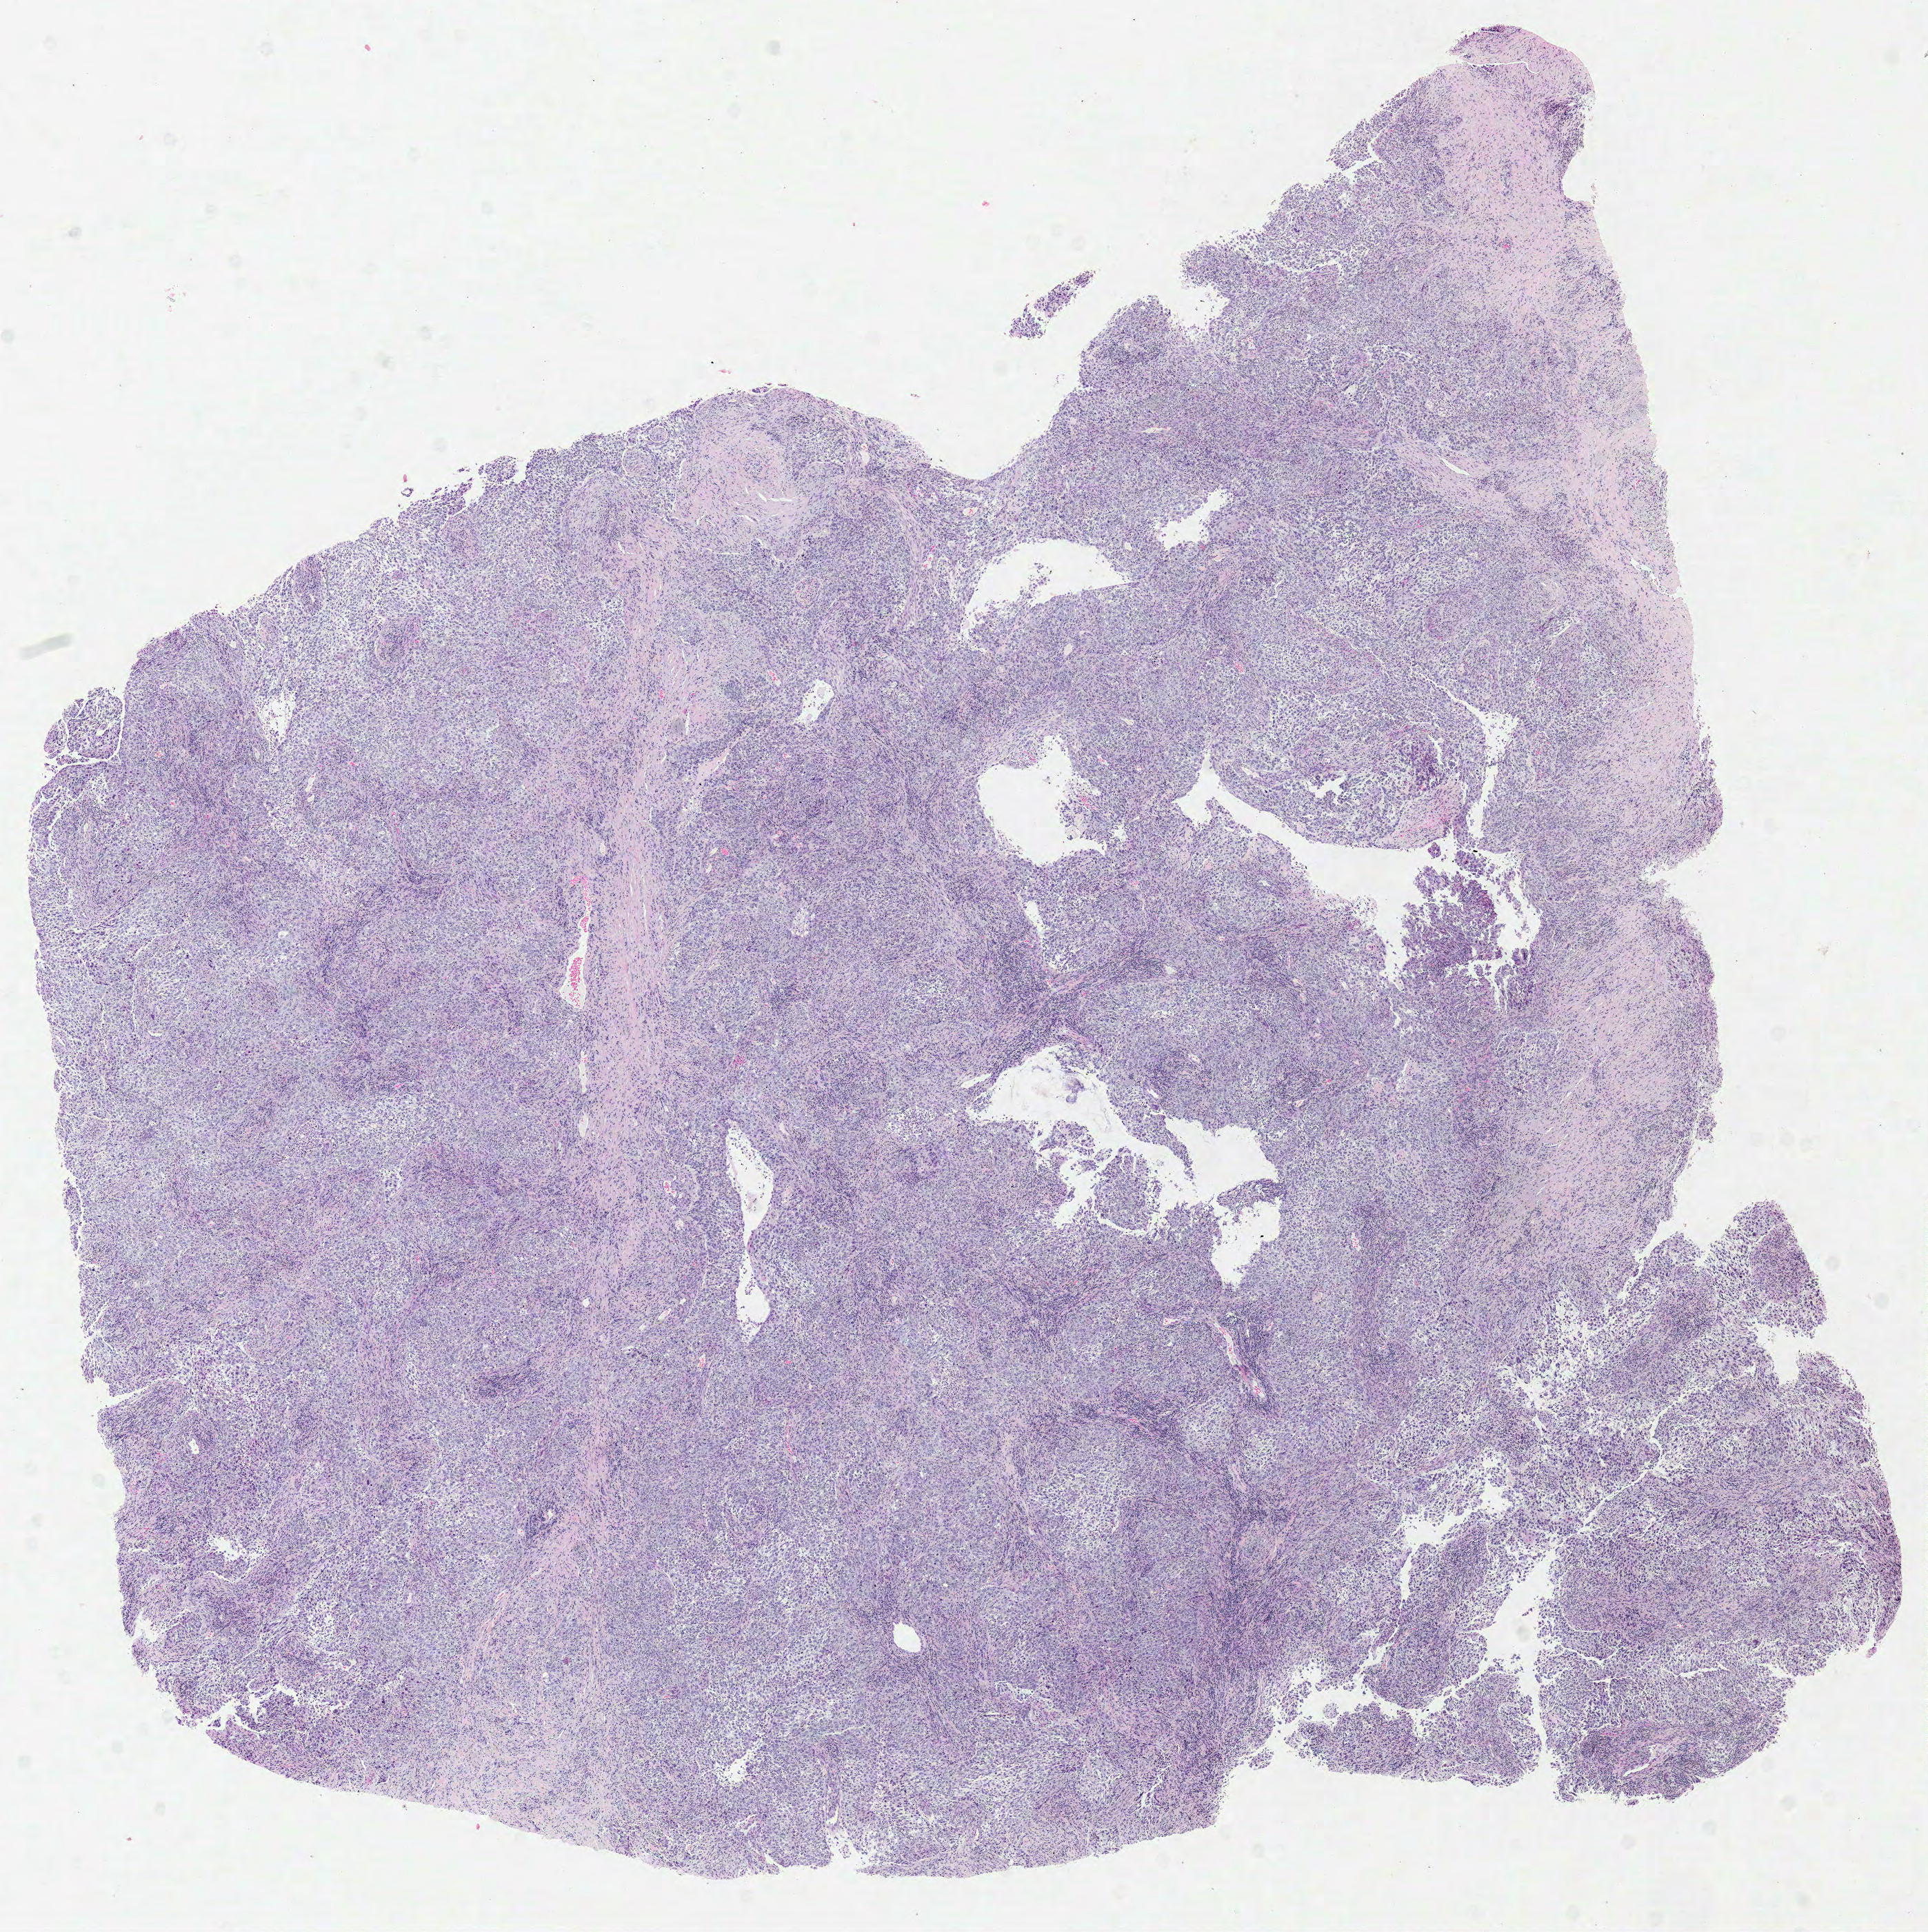
H&E whole-slide image — shown as a low-resolution overview of the whole scanned area (about 11.0 x 11.0 mm, slide scanned at 40x), formalin-fixed paraffin-embedded (FFPE) diagnostic section, primary tumour sample from the lung. Patient: male, age at initial diagnosis 63 years.
Laterality: right. AJCC pathologic stage: IB (5th edition). TNM: T2 N0 M0. Histologic diagnosis: Squamous cell carcinoma, NOS (upper lobe, lung).